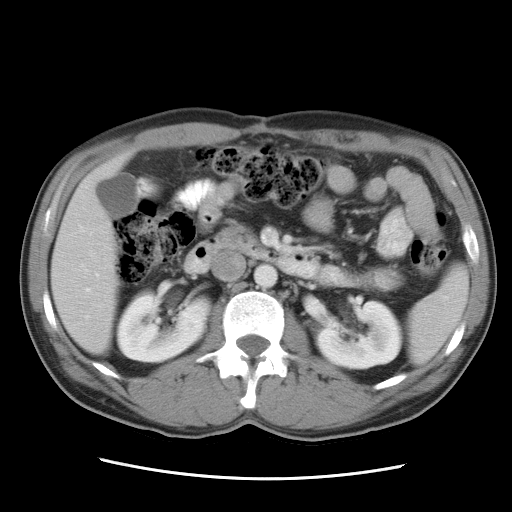
Contrast-enhanced abdominal CT, one axial slice. Position 12 of 34 along the scan axis. Reconstruction kernel STANDARD. Soft-tissue window (W 400 / L 40 HU). 7.5 mm slice thickness. 512 × 512 image matrix, field of view 360 × 360 mm. Male patient, age 40 years. From the clinical record (not read from this slice): diagnosis: colorectal cancer liver metastases, imaged before liver resection; multiple liver metastases: yes; largest metastasis: 1.5 cm; chemotherapy before resection: no.
Structures marked on this image (expert manual segmentation):
- liver: bounding box [x1, y1, x2, y2] px = [51, 157, 127, 352]
- planned liver remnant (the part of the liver to remain after resection): [51, 157, 127, 353]
- portal vein (with intrahepatic branches): [86, 234, 97, 292]